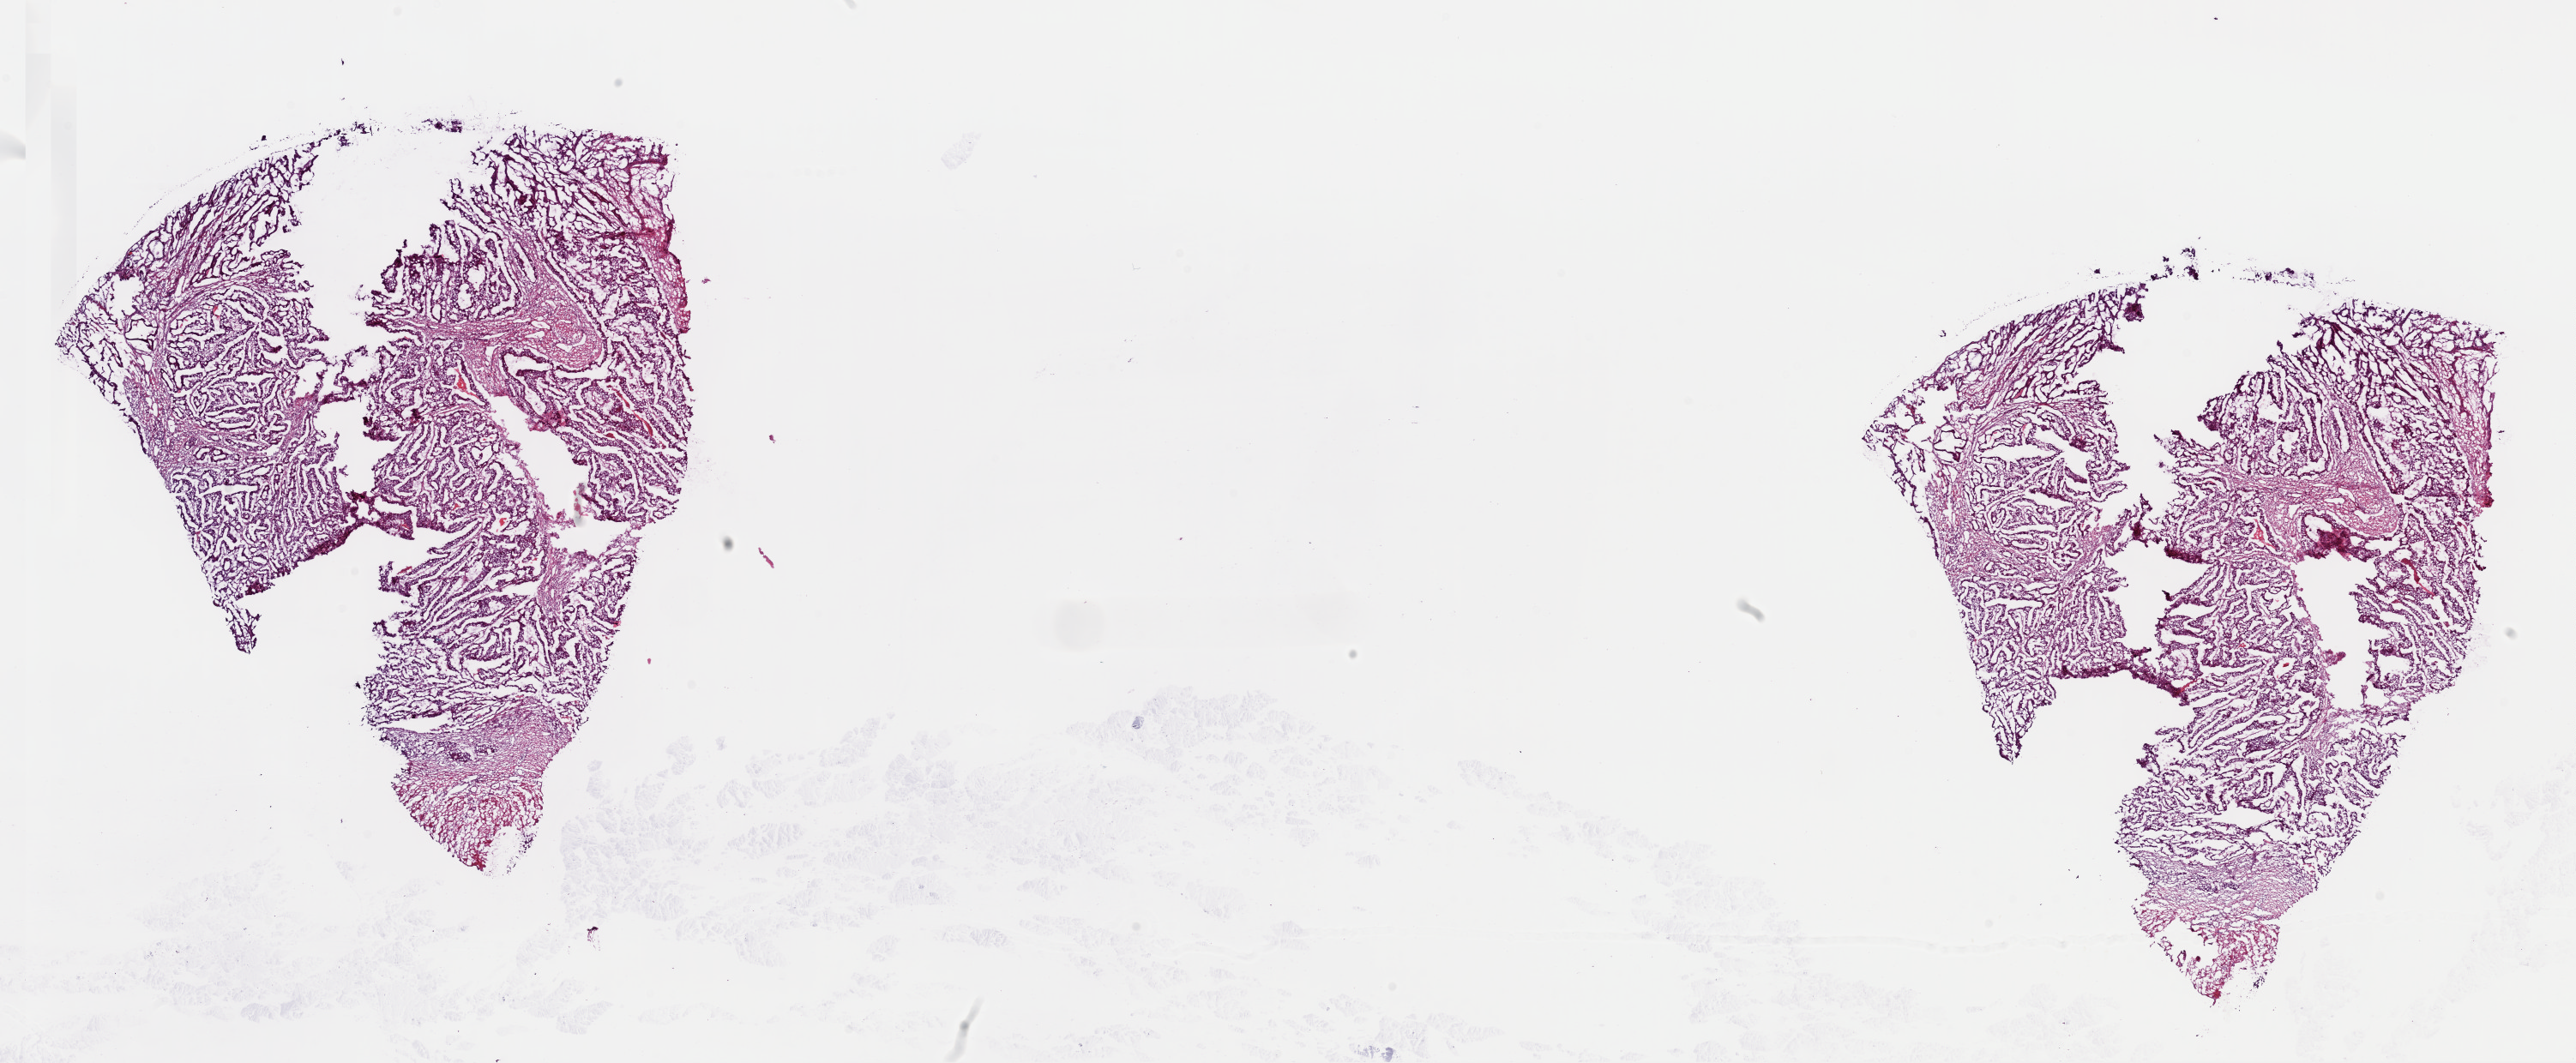
Digitized H&E-stained tissue section (whole slide), shown as a low-resolution overview of the whole scanned area (about 23.7 x 9.8 mm, acquisition: 40x scan); frozen section from the top of the tissue portion; sample: primary tumour, colon. Male, age 74 years at initial diagnosis.
Pathologic diagnosis: Adenocarcinoma, NOS (sigmoid colon).